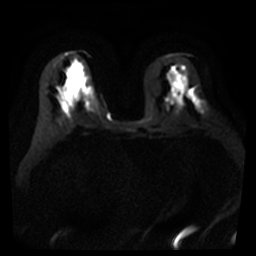
Breast MRI, one axial slice. Slice 20 of 40 in the series (ordered by position). Diffusion-weighted series; image 2 of 4 stored at this slice position (different b-values; order by instance number). 3 T. 256 × 256 image matrix, field of view 360 × 360 mm. Female patient.
Annotated regions visible in this slice (expert manual segmentation):
- tumour on diffusion-weighted imaging: bounding box [x1, y1, x2, y2] px = [200, 103, 206, 110]